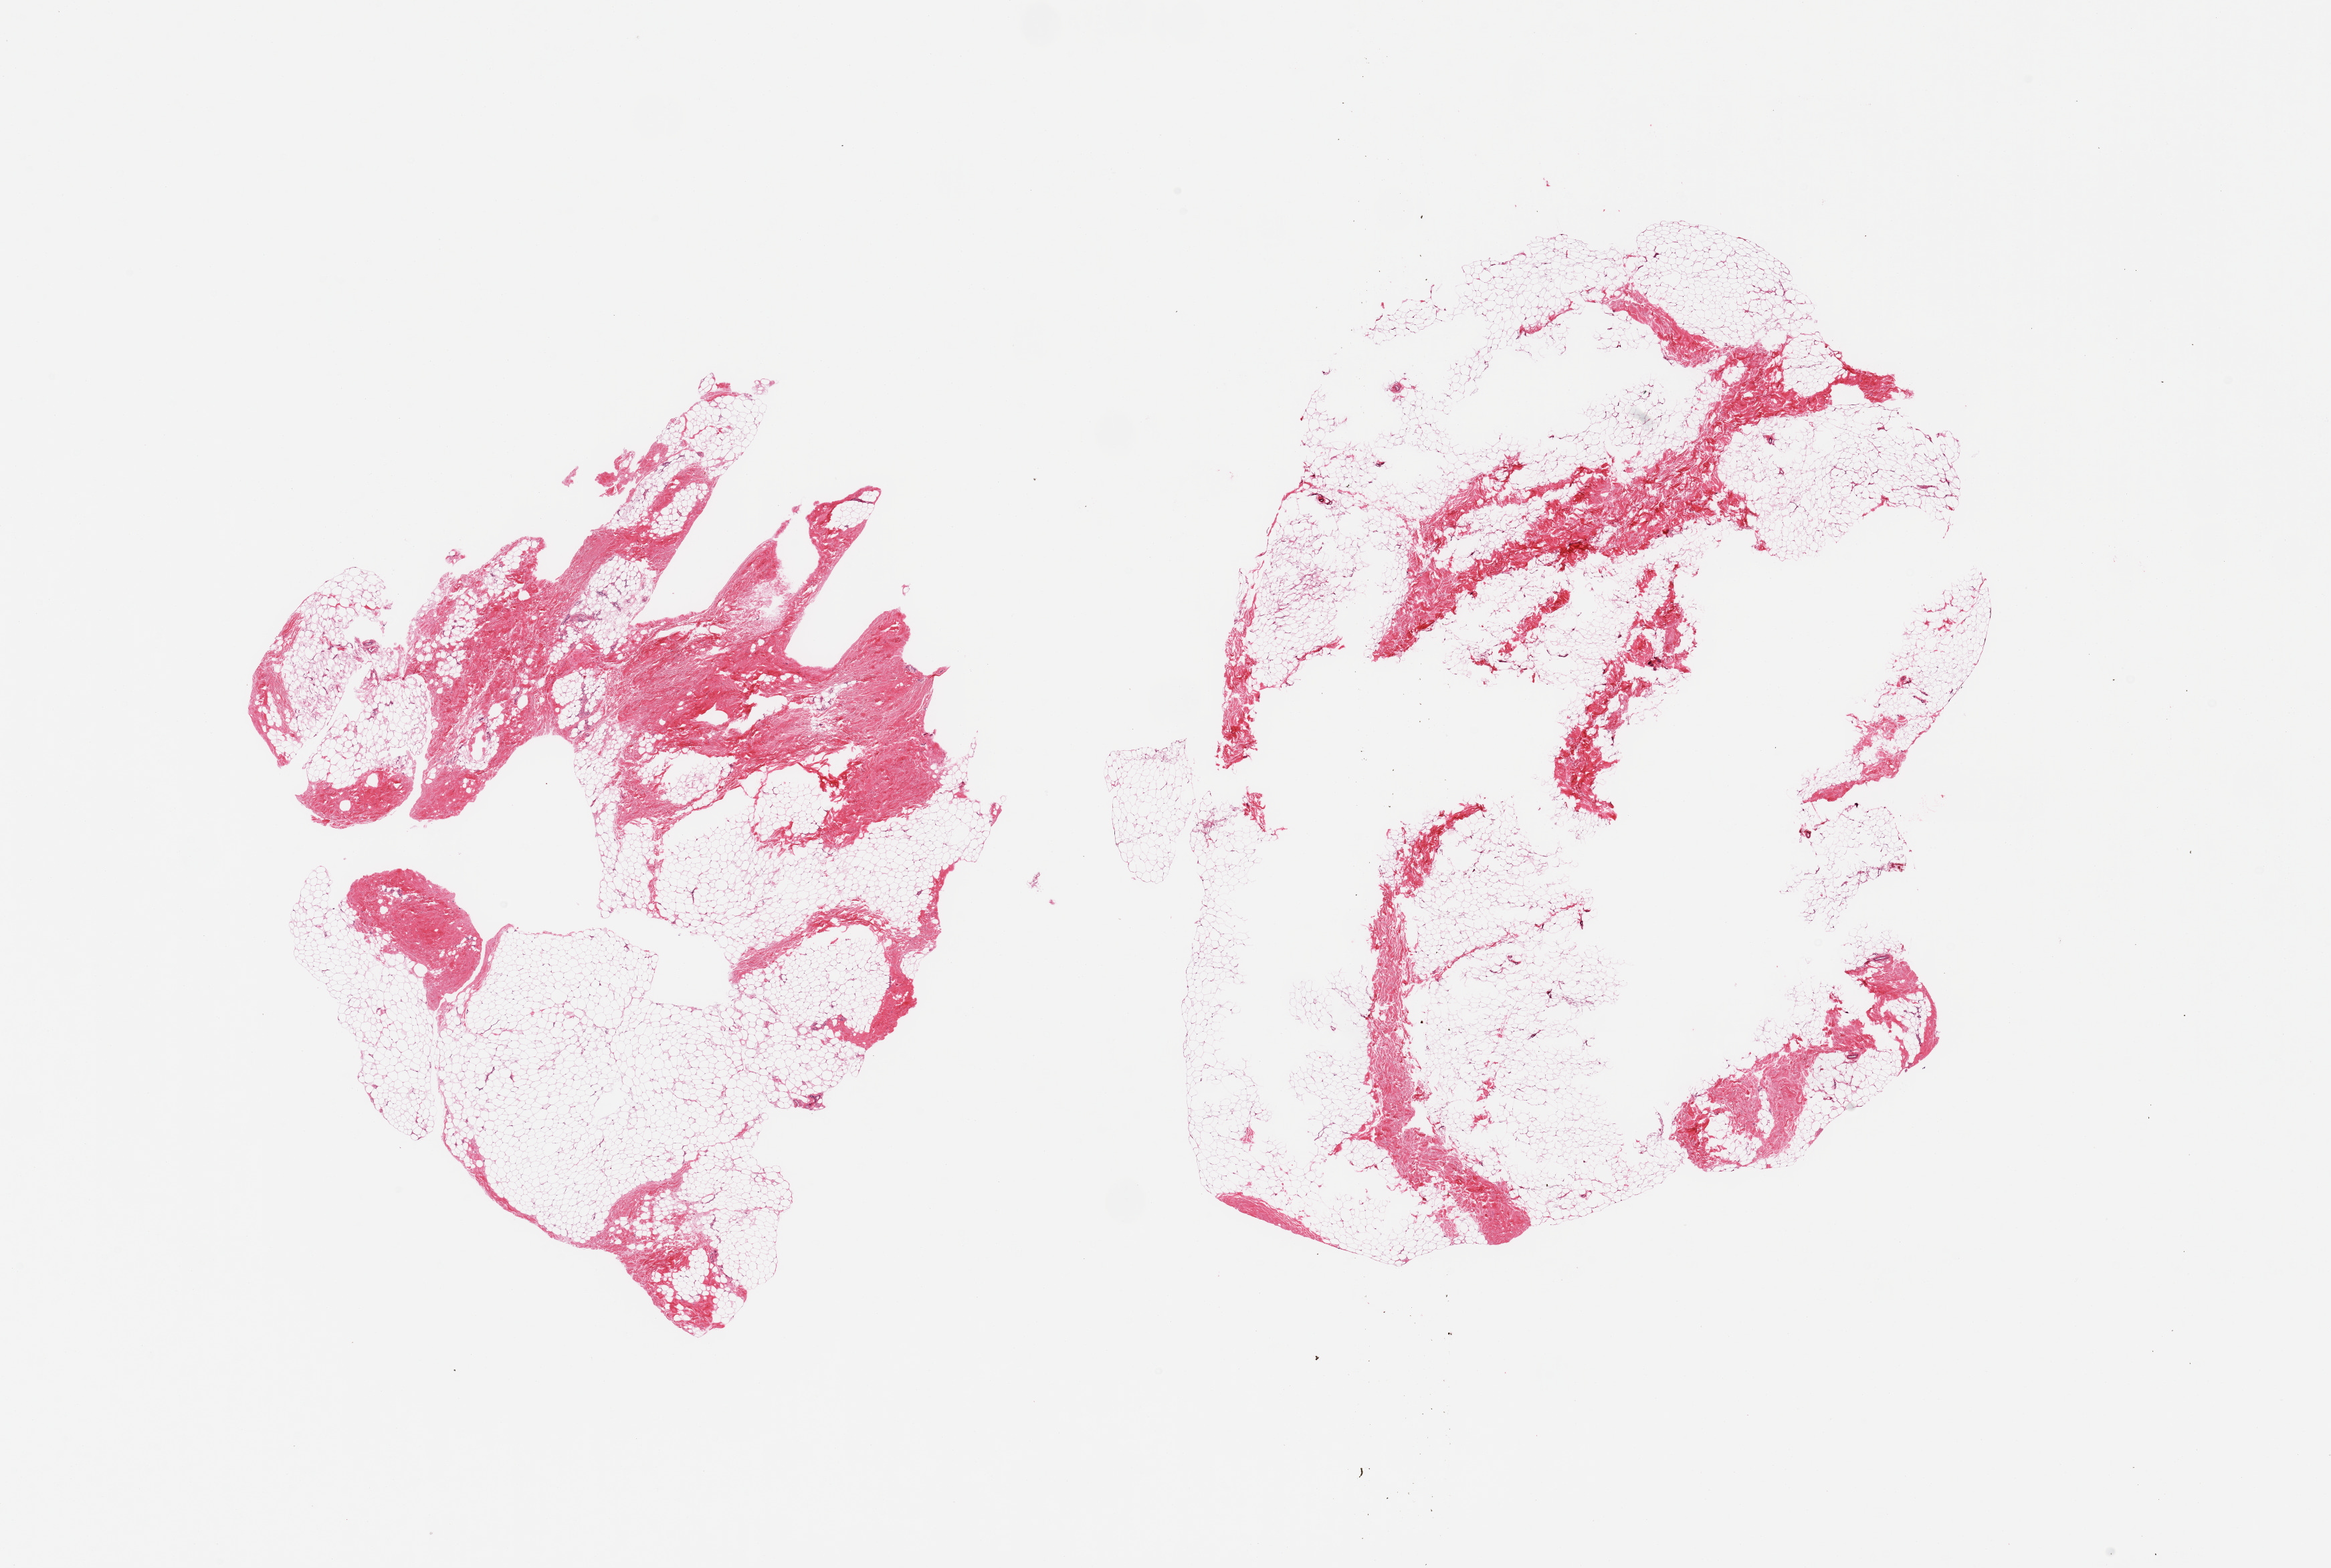
Digitized hematoxylin and eosin (H&E)-stained section, brightfield — shown as a low-resolution overview of the whole scanned area (about 27.6 x 18.5 mm, acquisition: 20x scan); PAXgene-fixed, paraffin-embedded tissue; sampled site (target tissue): breast; tissue donor sample. Donor: male.
Reviewer comment on this tissue sample: 2 pieces; fat admixed with dense fibrocollagenous tissue, no ductal elements seen, some central defects (? poor fixation).